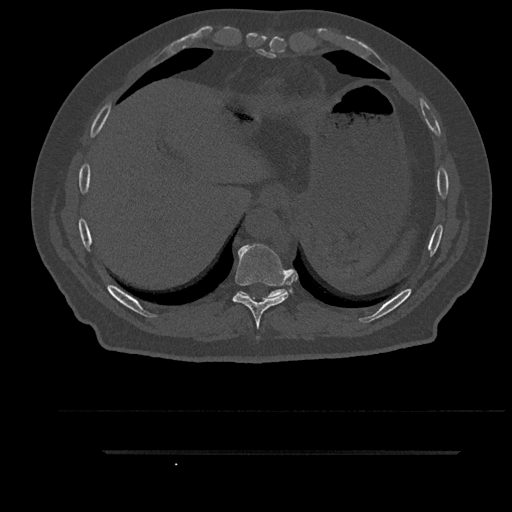
CT including the spine, one axial slice. Position 412 of 797 along the scan axis. Reconstruction kernel Br40s/3. 120 kVp. Bone window (W 1800 / L 400 HU). 0.5 mm slice thickness. 512 × 512 image matrix. Patient: male, 63 years. Case-level facts recorded for this patient, not image findings: primary cancer: renal; vertebrae with lytic lesions (as recorded): T8.
Structures marked on this image (semi-automatically segmented with operator editing):
- T10 vertebra: bounding box (x1, y1, x2, y2) in pixels: (237, 289, 286, 298)
- T9 vertebra: (232, 244, 291, 338)